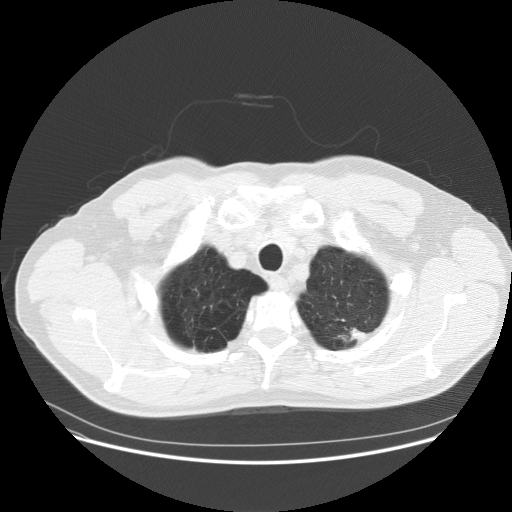
Low-dose screening chest CT, axial slice, first (baseline) screen, lung window (W 1500 / L -600 HU), 2.5 mm slice thickness, slice 12 of 158 in the series, 512 × 512 image matrix, field of view 400 × 400 mm. Male, age 61 years at enrolment. Current smoker at enrolment.
• Expert-annotated lung lesion, bounding box [x1, y1, x2, y2] px = [323, 308, 387, 360].
• Reader record for this screening exam (exam-level; its link to the box is not recorded): non-calcified nodule or mass ≥4 mm, left upper lobe, 12 × 6 mm, poorly defined margins, soft tissue attenuation.
• Official screen result: positive, change unspecified: nodule(s) >= 4 mm or enlarging nodule(s), mass(es), or other non-specific abnormalities suspicious for lung cancer.